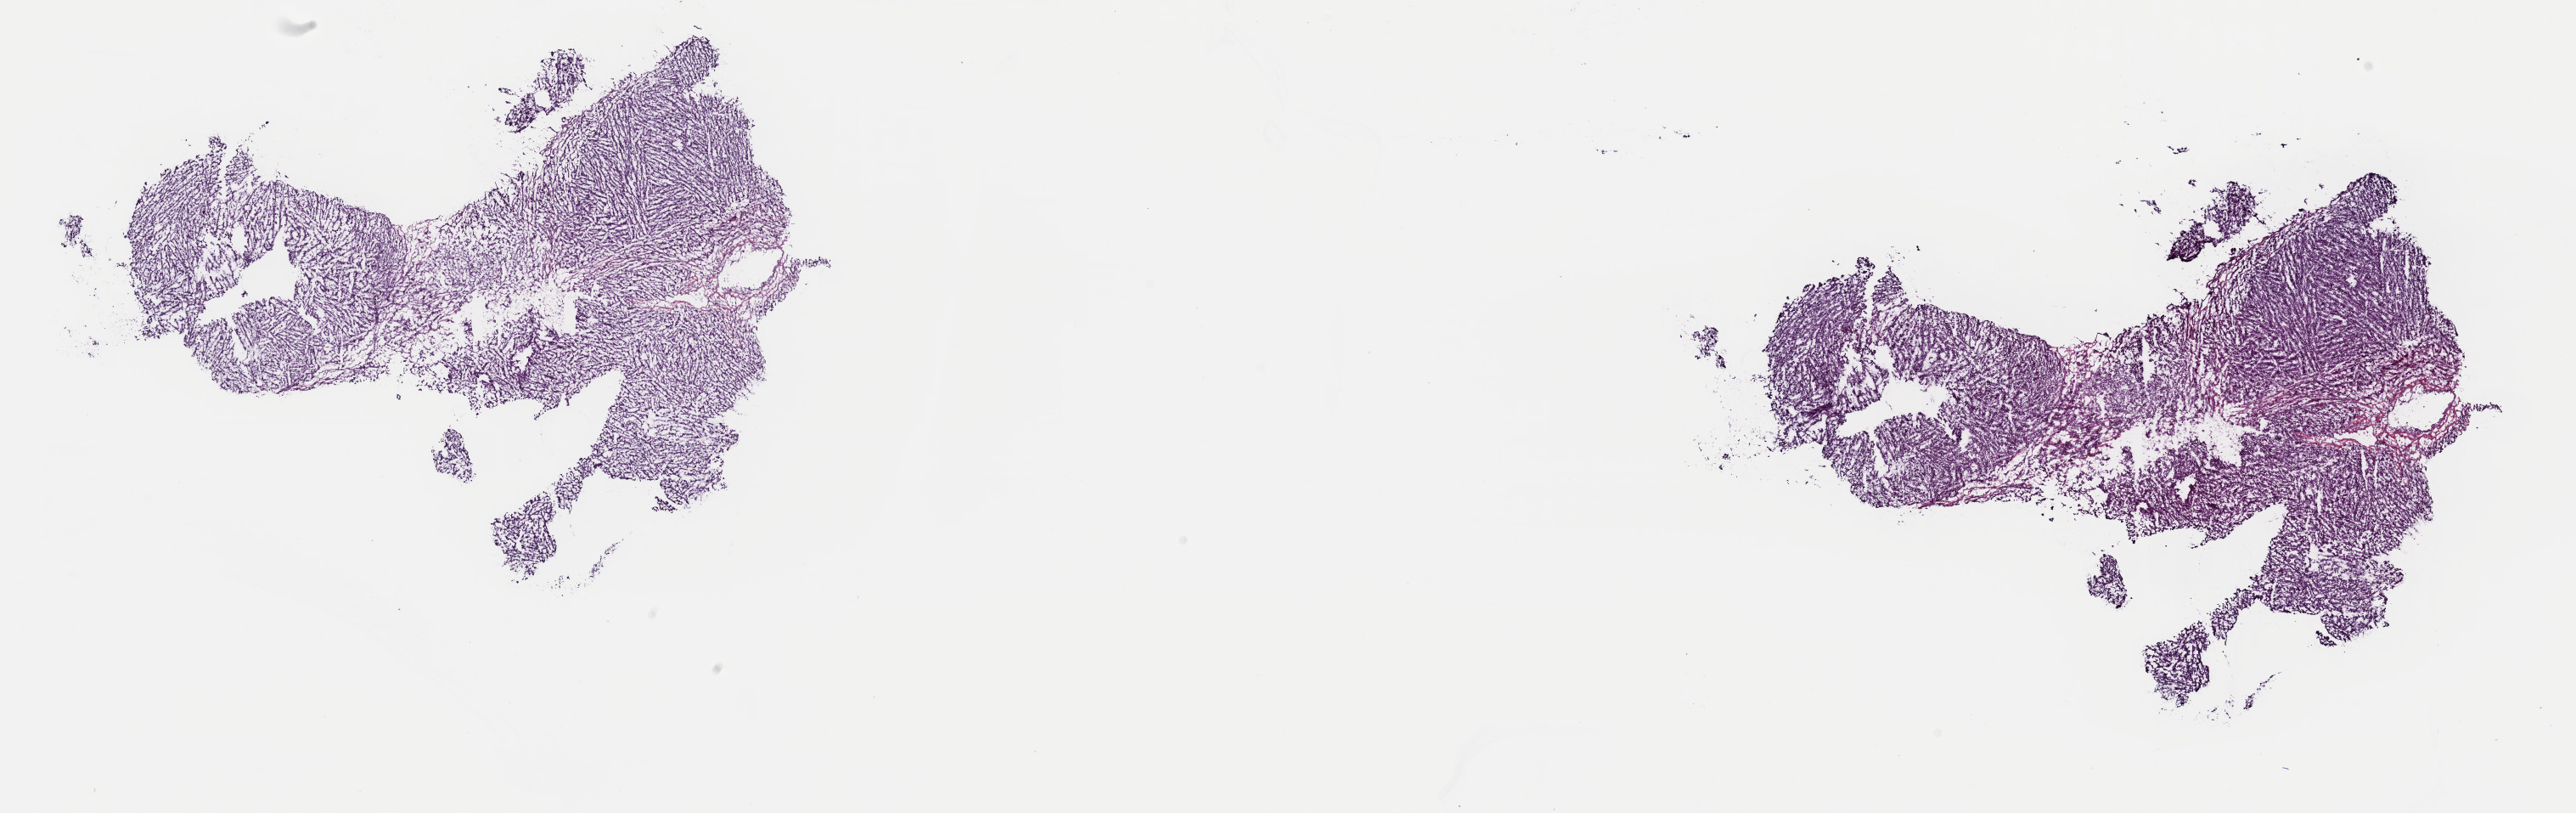
Whole-slide histology image, Hematoxylin and eosin (H&E) stained — a low-resolution overview of the entire scanned area, about 24.0 x 7.6 mm (from a 40x scan), frozen section from the top of the tissue portion, primary tumour sample from the adrenal cortex. Male, age 40 years at initial diagnosis. Pathologist review of this section (percent, as recorded): tumour cells 100%, tumour nuclei 95%, normal cells 0%, stromal cells 0%, necrosis 0%. Infiltration values recorded for this section: lymphocyte infiltration 0%, monocyte infiltration 0%, neutrophil infiltration 0%.
Diagnosis: Adrenal cortical carcinoma (cortex of adrenal gland). Laterality: left.